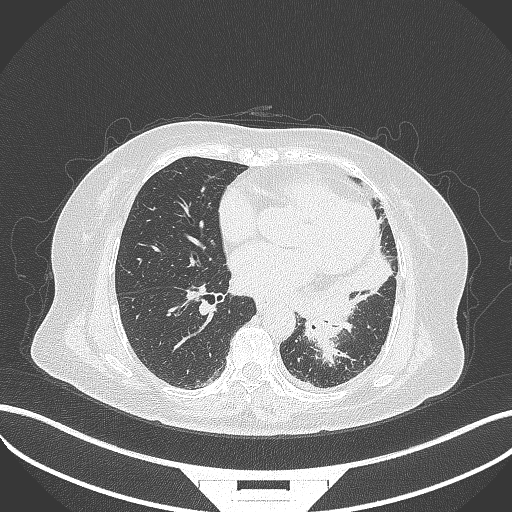
Chest CT, one axial slice. Position 154 of 322 along the scan axis. Reconstruction kernel B70f. 120 kVp. Lung window (W 1500 / L -600 HU). 1 mm slice thickness. 512 × 512 image matrix. Patient: female, 69 years. From the clinical record (not read from this slice): clinical TNM (as recorded): T2b N3 M1.
Outlined on this slice (rectangle marked by the reading radiologist):
- lung tumour (recorded histology: adenocarcinoma): bounding box [x1, y1, x2, y2] px = [300, 283, 350, 367]